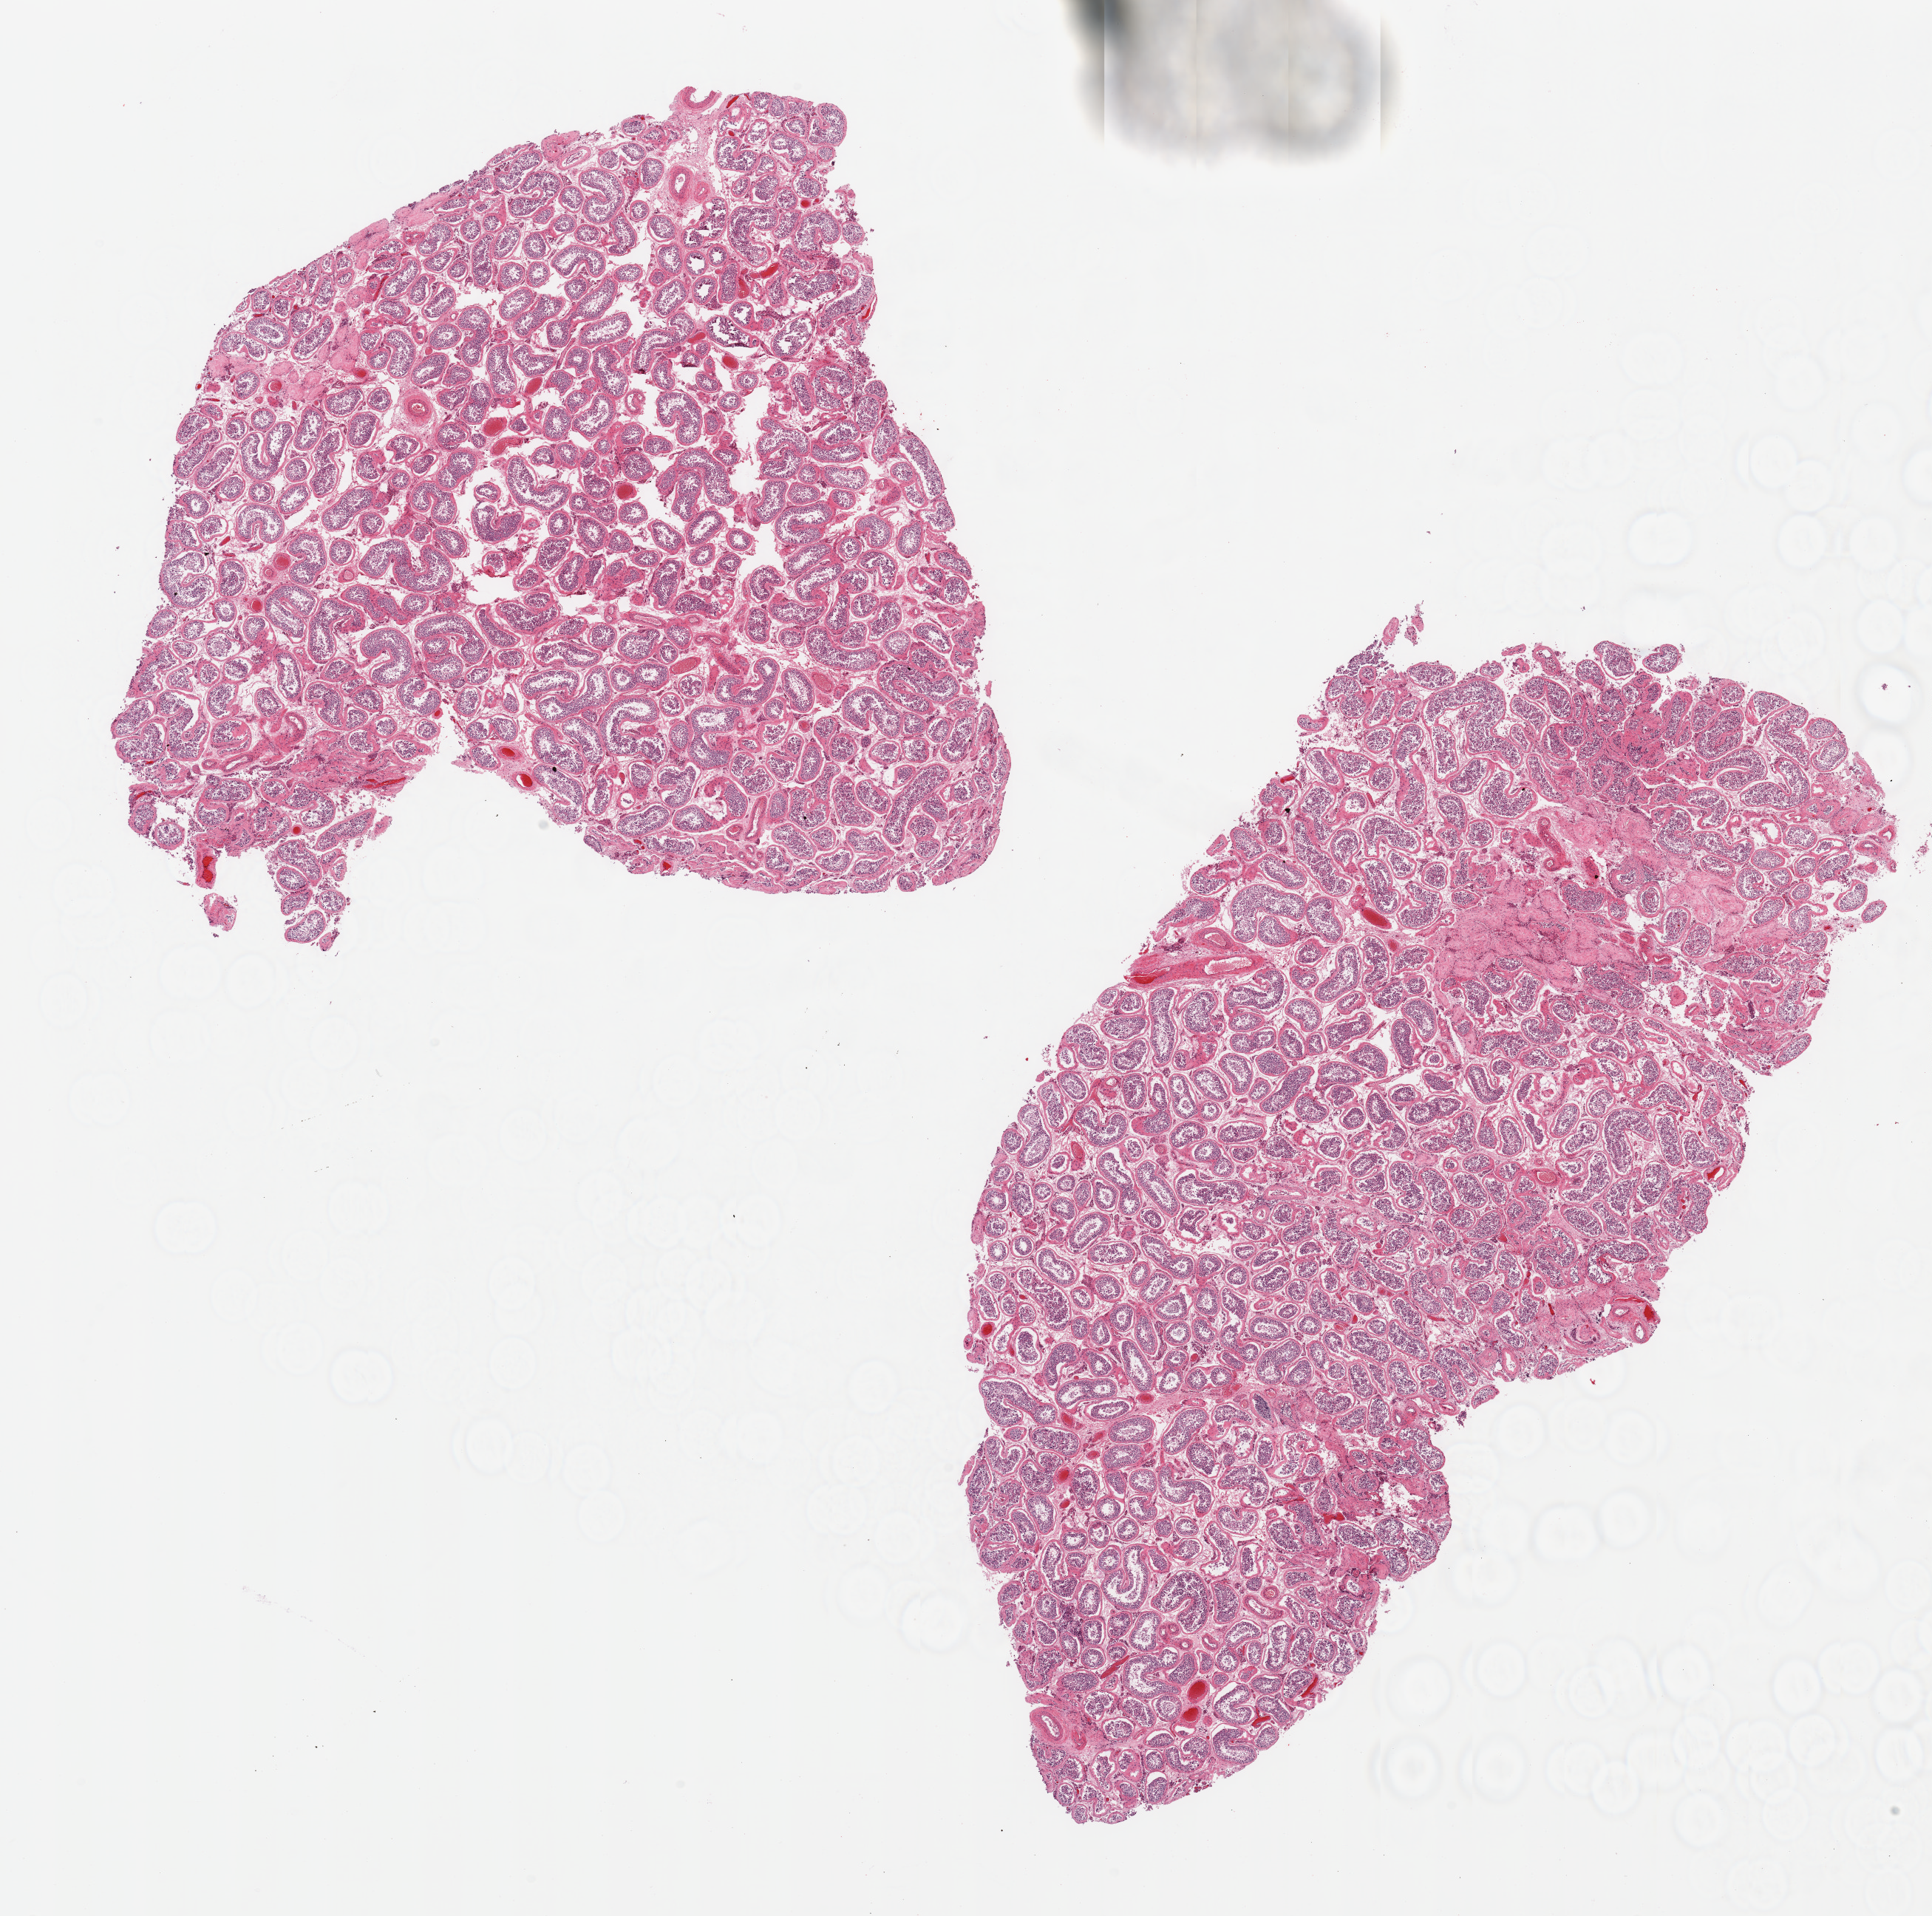
Digitized haematoxylin and eosin-stained section — whole scanned area (about 20.7 x 20.5 mm) shown as a low-resolution overview. PAXgene-fixed, paraffin-embedded tissue. Section of testis (target tissue). Donor tissue sample. Donor: male.
Reviewer comment on this tissue sample: 2 pieces; spermatogenesis present, some hyalinized tubules.